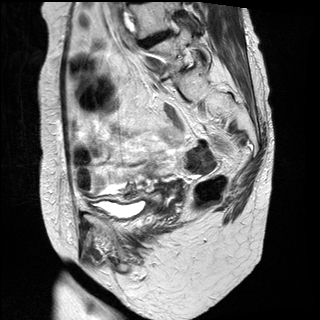
Pelvic MRI for cervical cancer, one sagittal slice. Slice 11 of 31 in the series (ordered by position). T2-weighted. 1.5 T. TE 89 ms, TR 3890 ms. 320 × 320 image matrix, field of view 260 × 260 mm. Patient: female, 61 years.
Outlined on this slice (manually delineated by an expert):
- uterus and cervix: bounding box [x1, y1, x2, y2] px = [153, 176, 186, 218]